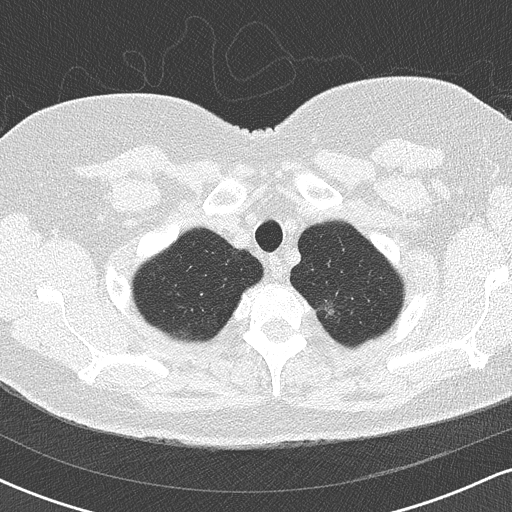
Chest CT (low-dose screening protocol), one axial image. Third screening round (two years after baseline). Lung window (W 1500 / L -600 HU). 2 mm slice thickness. Lung (sharp) reconstruction kernel (B50f). 120 kVp. Slice 22 of 170 in the series. Female, age 60 years at enrolment. Former smoker at enrolment.
Lesion marked by an expert reader, bounding box [x1, y1, x2, y2] px = [298, 287, 353, 336]. The exam's reader record, not a measurement of the box and not confirmed to be the same lesion: non-calcified nodule or mass ≥4 mm, left upper lobe, 10 × 10 mm, soft tissue attenuation, pre-existing on the prior screen: yes. Official screen result: positive, no significant change: stable abnormalities potentially related to lung cancer, unchanged since the prior screening exam.